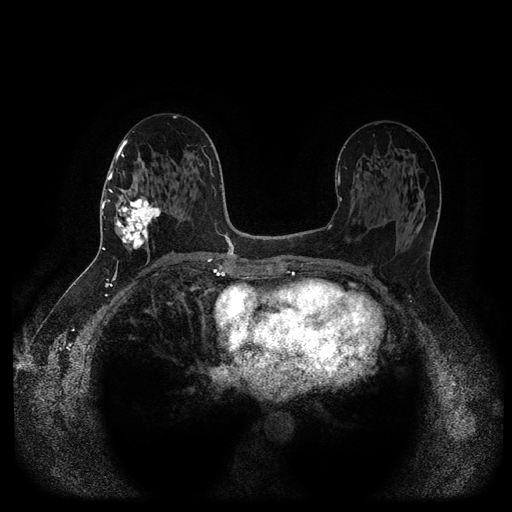
Breast MRI (dynamic contrast-enhanced, multi-phase), one axial slice. Slice 53 of 116 in the series (ordered by position). Dynamic contrast-enhanced series, time point 2 of 5 at this slice position (early post-contrast). 1.5 T. TE 2.6 ms, TR 5.3 ms. 2 mm slice thickness. 512 × 512 image matrix. Patient: female, 58 years.
Structures marked on this image (semi-automatic segmentation, software-assisted and operator-edited):
- breast lesion (labelled 'tumour' in the annotation; benign lesions carry a separate 'benign' label): bounding box [x1, y1, x2, y2] px = [112, 187, 164, 254]